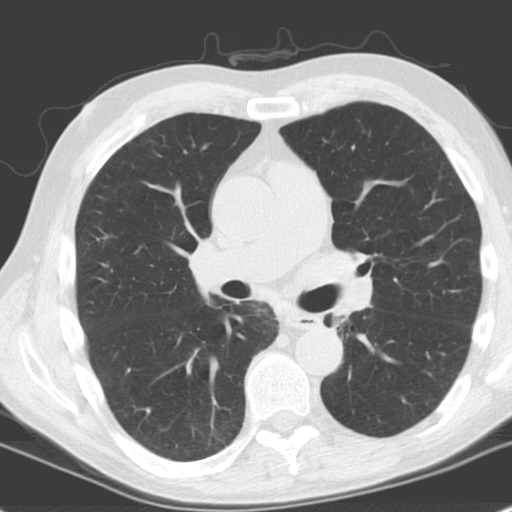
Low-dose screening chest CT, axial slice. Baseline screening round. Lung window (W 1500 / L -600 HU). 3.2 mm slice thickness. Standard (soft-tissue) reconstruction kernel (C). Slice 80 of 185 in the series. 512 × 512 image matrix. Male participant, aged 61 years at enrolment.
Expert reader's lesion annotation, bounding box (x1, y1, x2, y2) in pixels: (311, 306, 358, 343). No non-calcified nodule or mass ≥4 mm was recorded by the screening reader at this exam. Participant outcome: lung cancer diagnosed 1146 days after this screen — squamous cell carcinoma, NOS, left upper lobe, left lower lobe, well differentiated (G1), stage IIB (AJCC 6th edition), 100 mm at pathology.